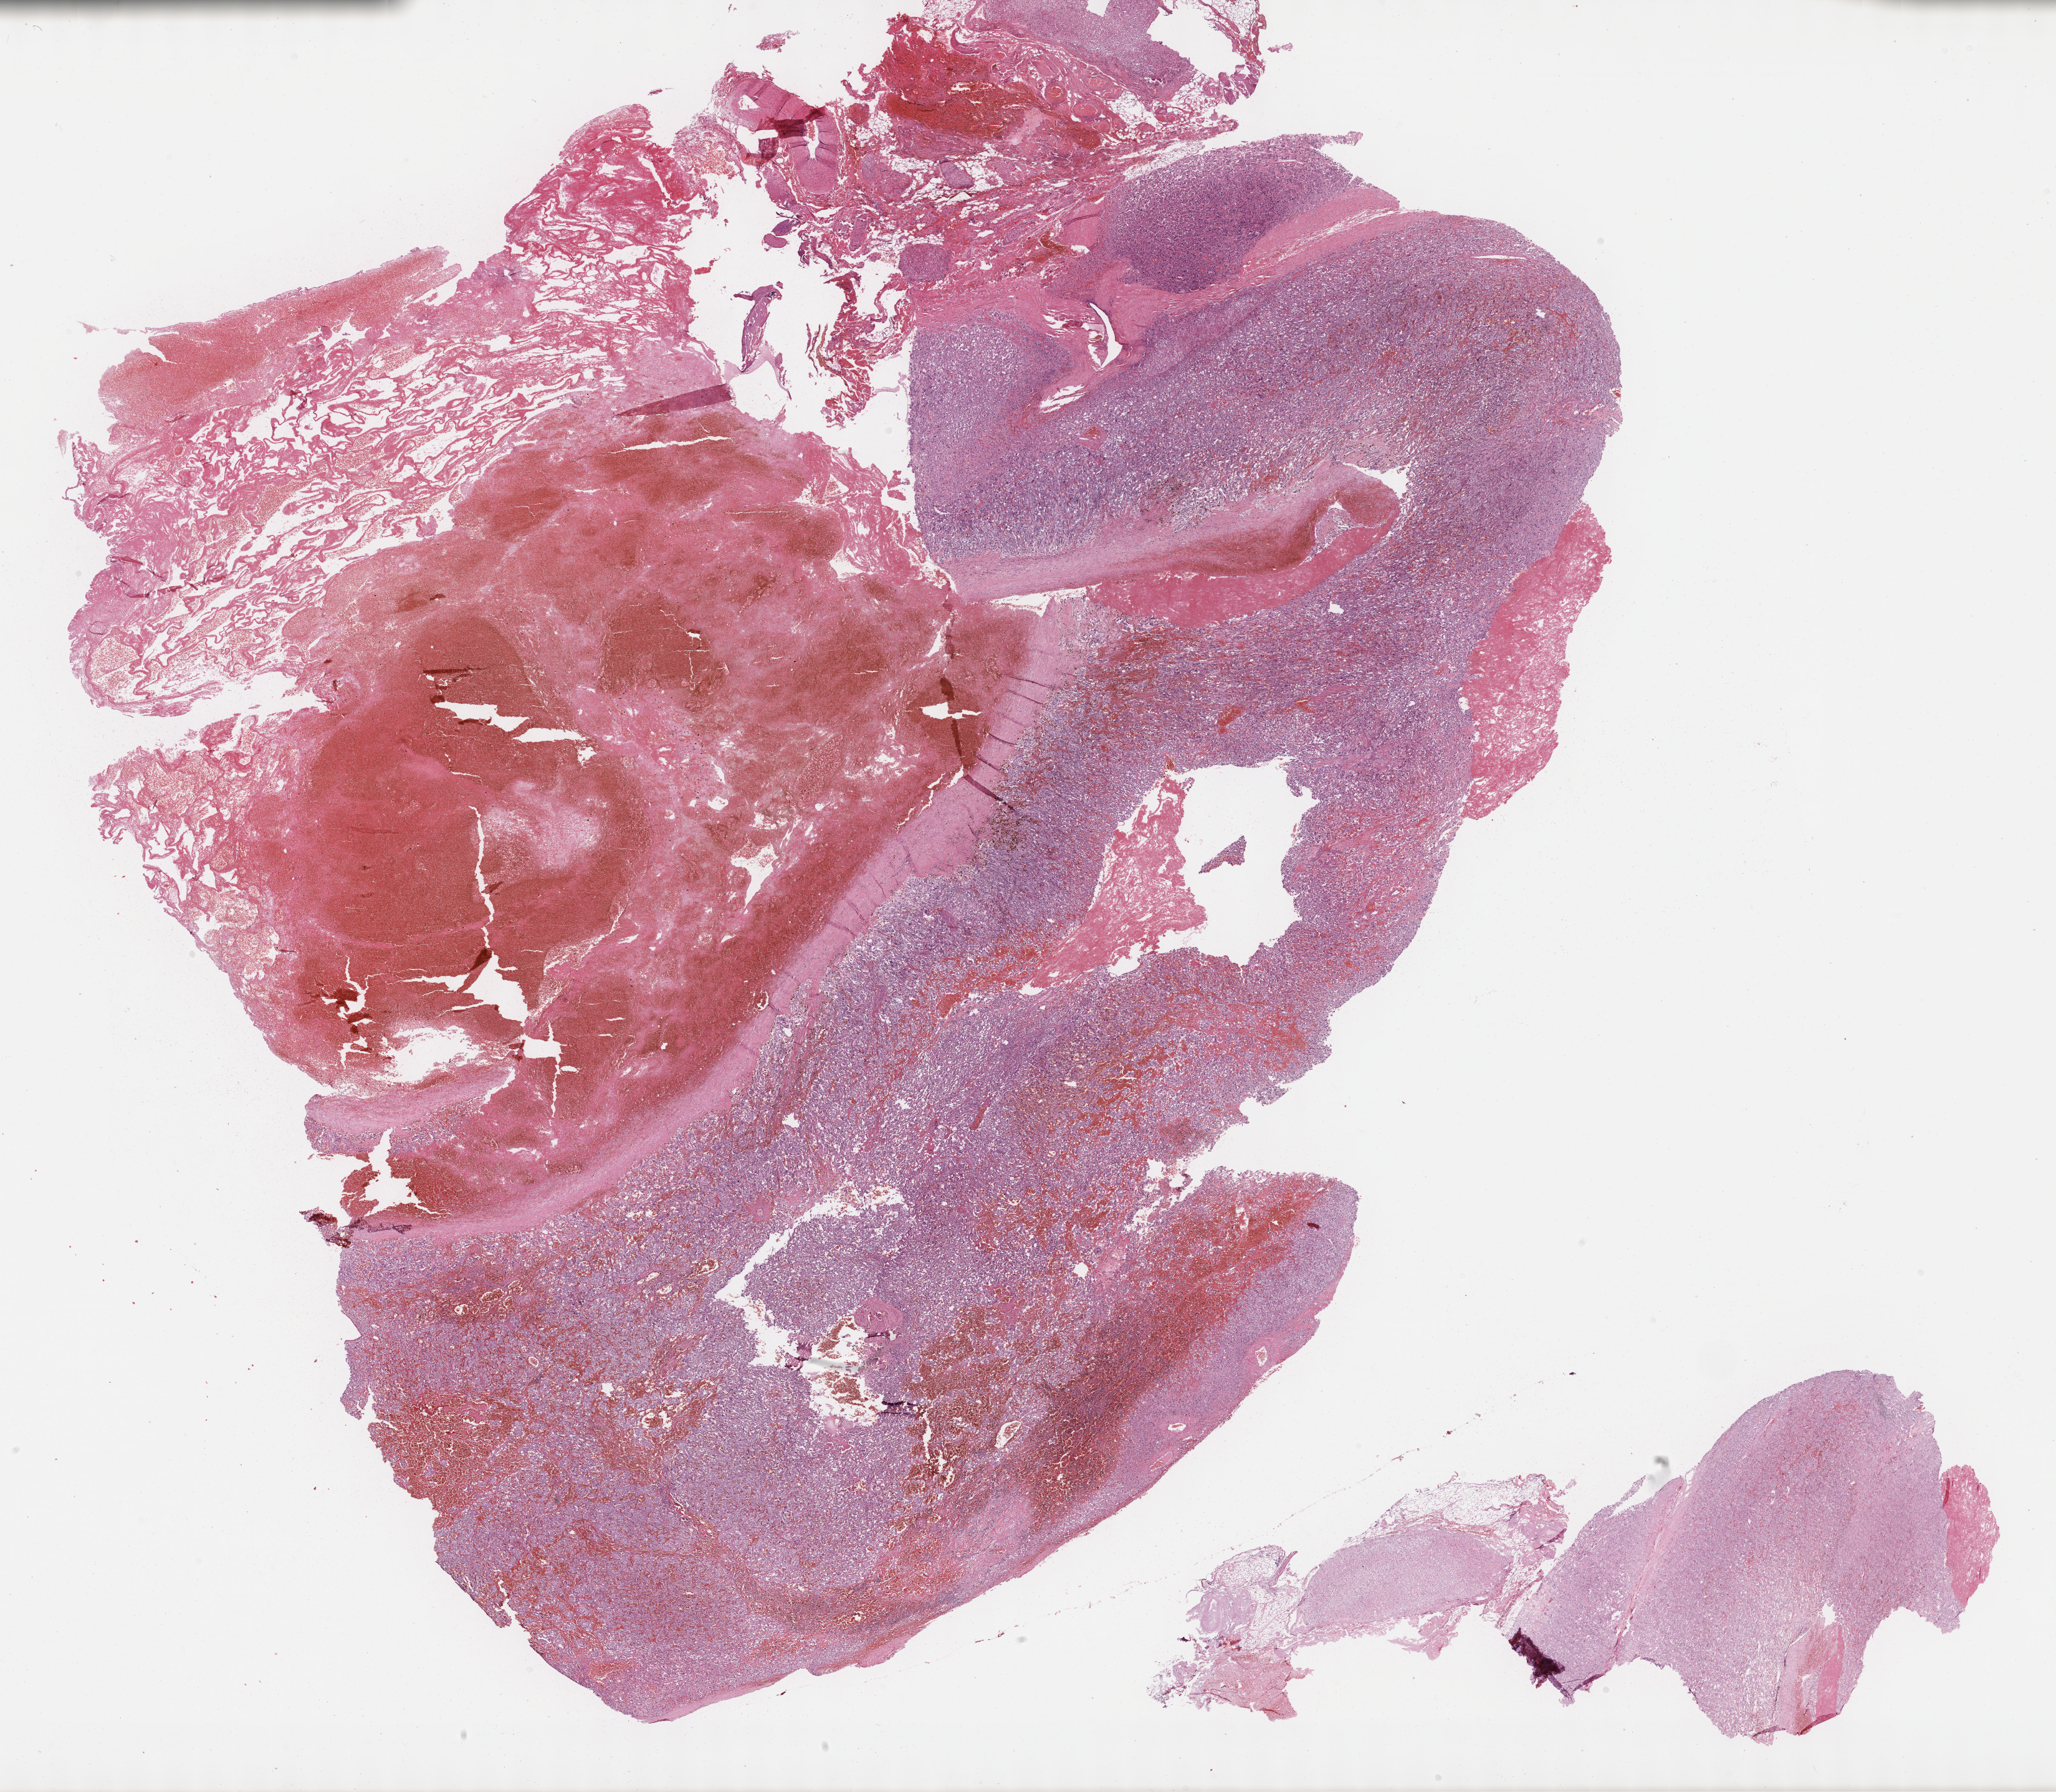
Whole-slide histology image, H&E-stained — a low-resolution overview of the entire scanned area, about 26.7 x 23.3 mm, formalin-fixed paraffin-embedded (FFPE) diagnostic section, sample: primary tumour, adrenal gland. Female, age 76 years at initial diagnosis.
Histologic diagnosis: Pheochromocytoma, NOS. Laterality: right.